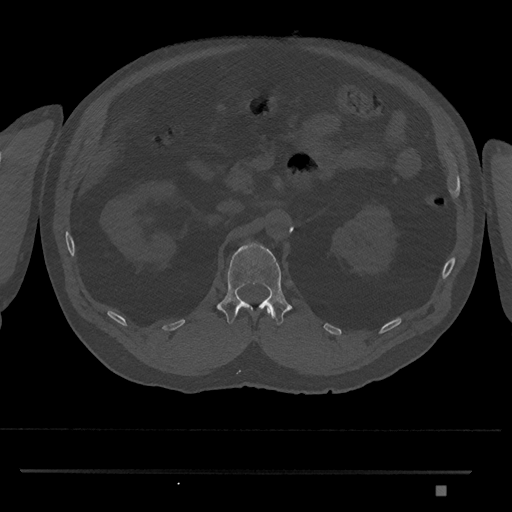
CT including the spine, one axial slice. Position 832 of 1134 along the scan axis. Reconstruction kernel Br40s/3. 120 kVp. Bone window (W 1800 / L 400 HU). 0.5 mm slice thickness. 512 × 512 image matrix, field of view 429 × 429 mm. Male patient, age 65 years. Case-level facts recorded for this patient, not image findings: primary cancer: prostate.
Structures marked on this image (semi-automatically segmented with operator editing):
- L1 vertebra: bounding box (x1, y1, x2, y2) in pixels: (217, 242, 292, 325)
- T12 vertebra: (267, 309, 272, 316)